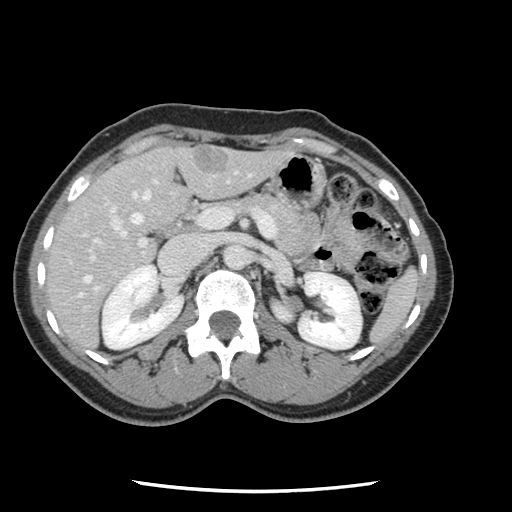
Contrast-enhanced abdominal CT, one axial slice. Slice 62 of 134 in the series (ordered by position). Intravenous contrast given. Soft-tissue window (W 400 / L 40 HU). 2.5 mm slice thickness. 512 × 512 image matrix, field of view 330 × 330 mm. Female patient, age 43 years. From the clinical record (not read from this slice): diagnosis: colorectal cancer liver metastases, imaged before liver resection; multiple liver metastases: yes; largest metastasis: 3.4 cm; chemotherapy before resection: no.
Annotated regions visible in this slice (expert manual segmentation):
- hepatic veins: bounding box (x1, y1, x2, y2) in pixels: (79, 180, 156, 297)
- liver: (46, 146, 288, 350)
- planned liver remnant (the part of the liver to remain after resection): (47, 150, 185, 311)
- portal vein (with intrahepatic branches): (83, 171, 278, 310)
- liver metastasis: (194, 151, 230, 173)